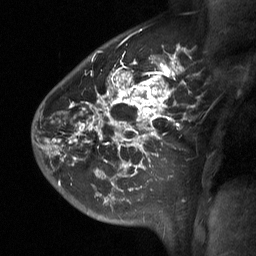
Breast MRI (dynamic contrast-enhanced), one sagittal slice. Position 46 of 64 along the scan axis. Dynamic contrast-enhanced study with each time point stored as its own series, time point 2 of 3 at this slice position (early post-contrast, ordered by acquisition time). 1.5 T. TE 4.8 ms, TR 27 ms. 2 mm slice thickness. 256 × 256 image matrix, field of view 200 × 200 mm. Female patient, age 42 years. From the clinical record (not read from this slice): setting: breast cancer imaged before/during neoadjuvant chemotherapy; receptor status: triple-negative.
Structures marked on this image (semi-automatic segmentation, software-assisted and operator-edited):
- analysis volume of interest (the breast-tissue region the enhancement analysis was run in; not a lesion): bounding box [x1, y1, x2, y2] px = [49, 45, 192, 197]
- tumour enhancement mask (voxels above the 90 % enhancement threshold inside the analysis volume of interest): [49, 47, 184, 176]